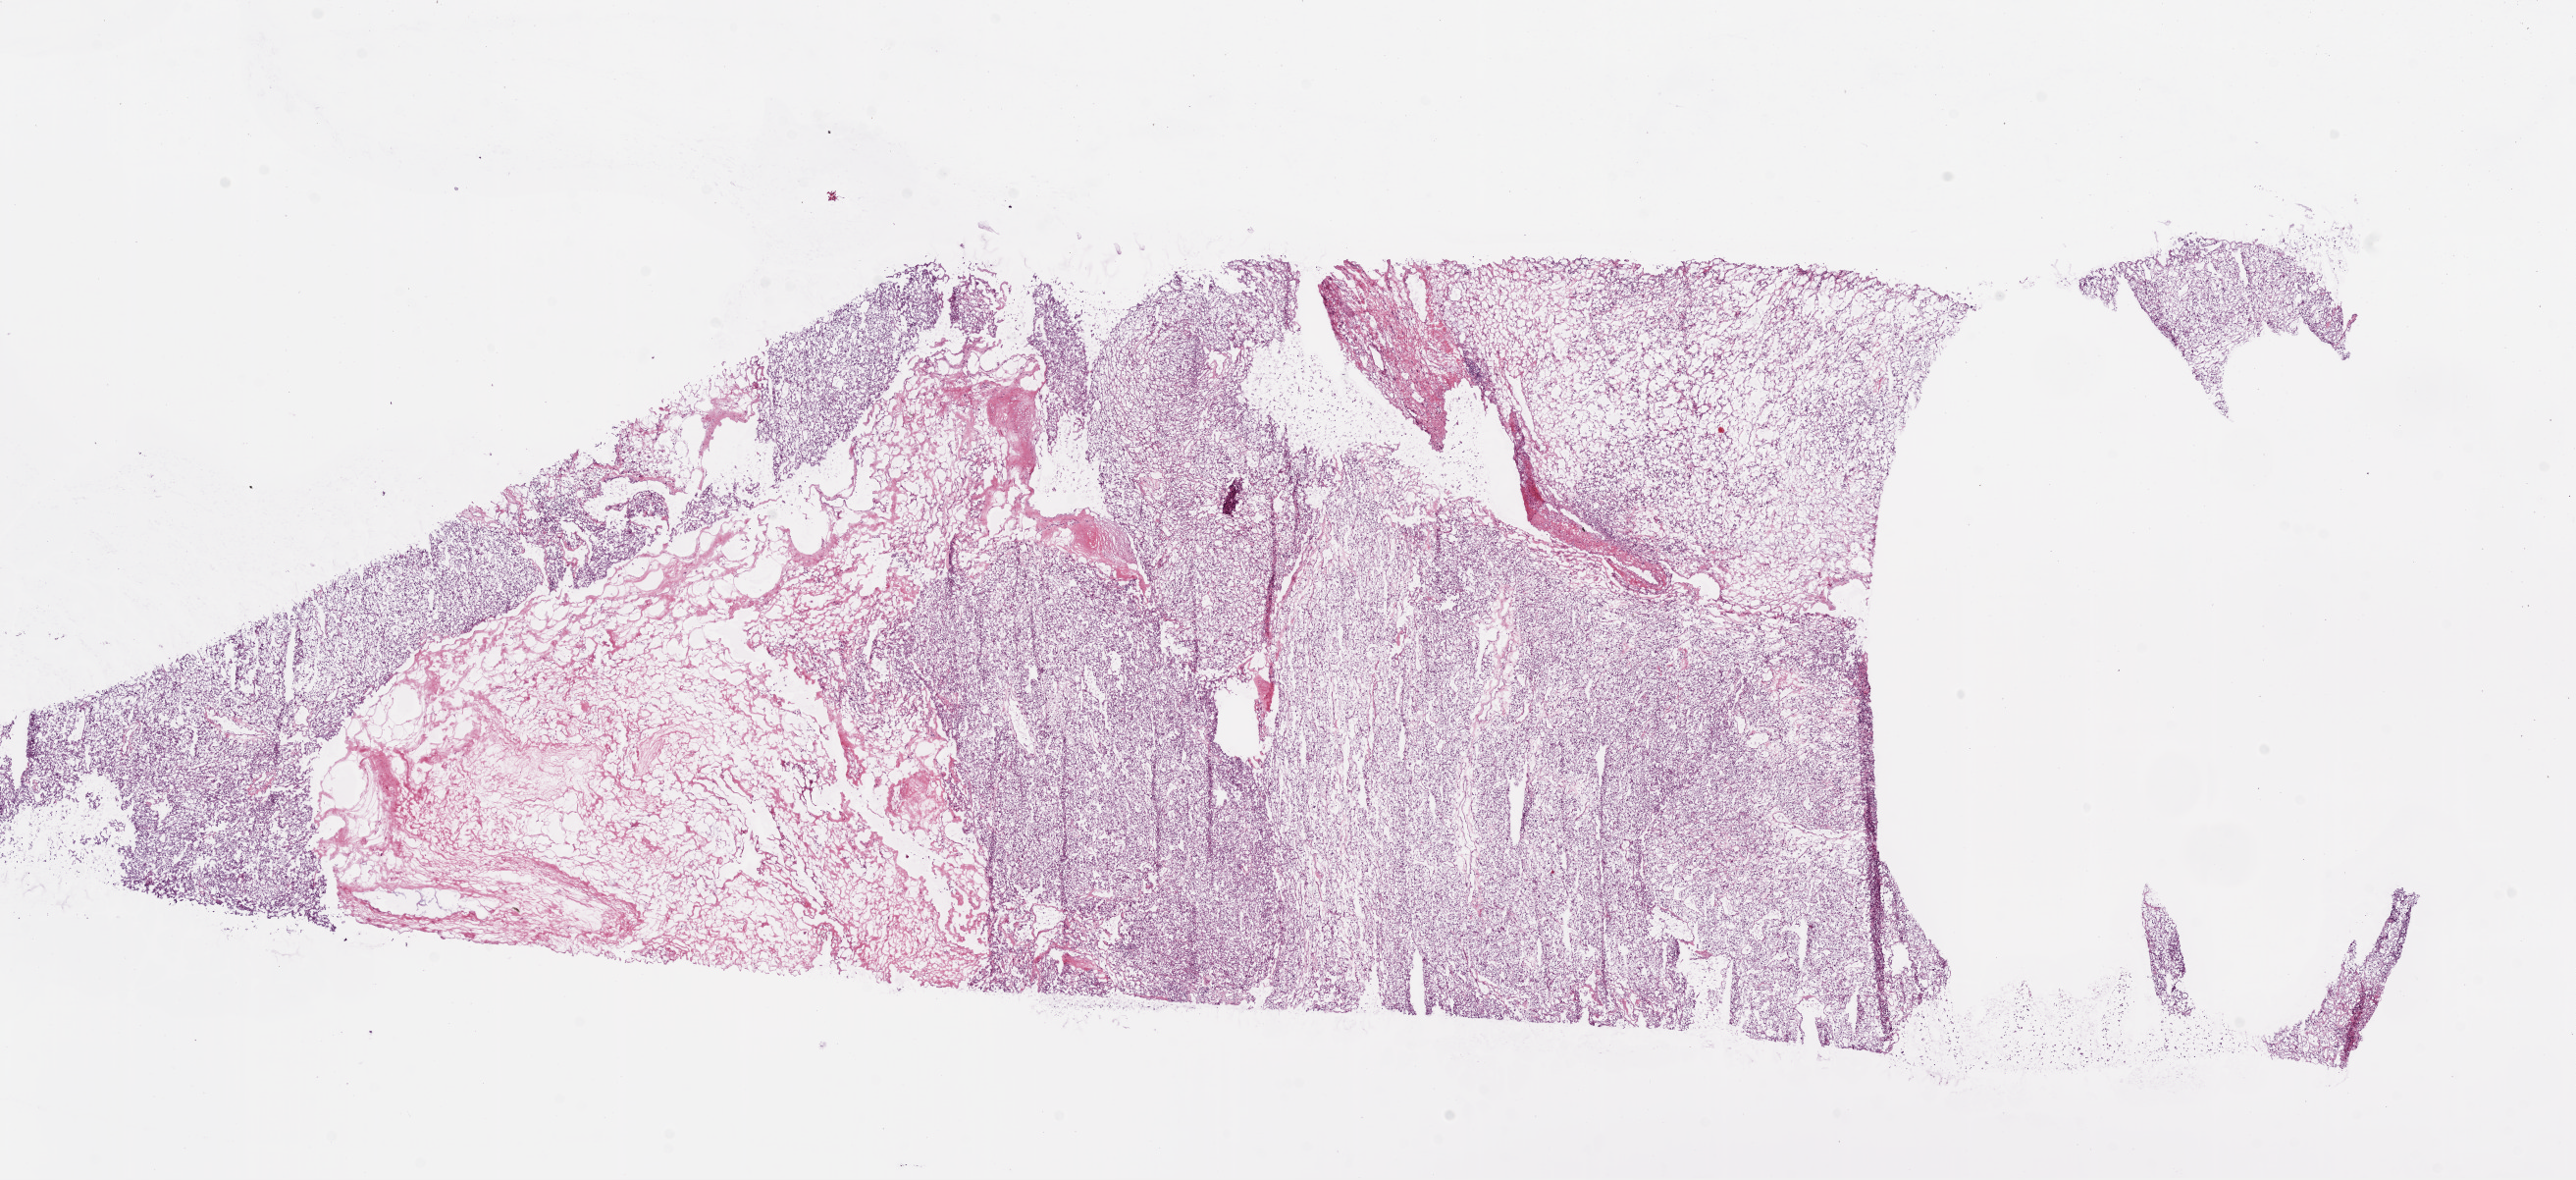
Hematoxylin and eosin (H&E) stained whole-slide image, low-resolution overview of the scanned area, about 21.1 x 9.6 mm (from a 20x scan). Frozen section from the bottom of the tissue portion. Primary tumour sample from the kidney. Patient: female, age at initial diagnosis 76 years. Histologic grade: G3 (poorly differentiated). Composition of this section per pathologist review: tumour cells 90%, tumour nuclei 85%, normal cells 0%, stromal cells 10%, necrosis 0%.
AJCC pathologic stage: I. Laterality: right. Histologic diagnosis: Clear cell adenocarcinoma, NOS.